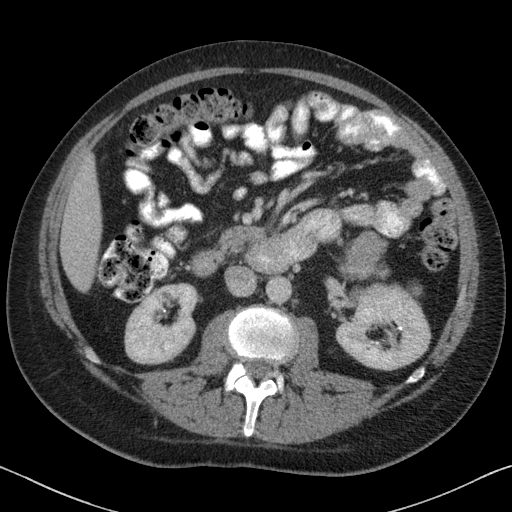
Contrast-enhanced abdominal CT, one axial slice. Position 31 of 88 along the scan axis. Reconstruction kernel B31f. 120 kVp. Intravenous contrast given. Soft-tissue window (W 400 / L 40 HU). 3 mm slice thickness. 512 × 512 image matrix, field of view 366 × 366 mm. Patient: male, 51 years. From the clinical record (not read from this slice): diagnosis: adrenocortical carcinoma; tumour side: left adrenal; tumour size at pathology: 16.5 cm; Ki-67 index: 30 %; stage (as recorded): 2.
Outlined on this slice (semi-automatically segmented with operator editing):
- mass: box from (x=344, y=232) to (x=392, y=278) px